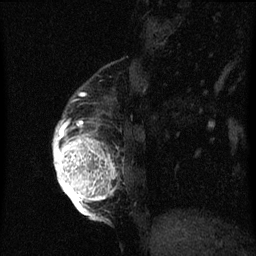
Breast MRI (dynamic contrast-enhanced), one sagittal slice. Position 14 of 60 along the scan axis. Dynamic contrast-enhanced series, image 2 of 3 at this slice position (ordered by acquisition). 1.5 T. TE 4.2 ms, TR 8 ms. 2 mm slice thickness. 256 × 256 image matrix. Patient: female, 56 years.
Outlined on this slice (semi-automatically segmented with operator editing):
- analysis volume of interest (the breast-tissue region the enhancement analysis was run in; not a lesion): box from (x=54, y=98) to (x=119, y=219) px
- tumour enhancement mask (voxels above the 70 % enhancement threshold inside the analysis volume of interest): (x=54, y=122)–(x=117, y=219)